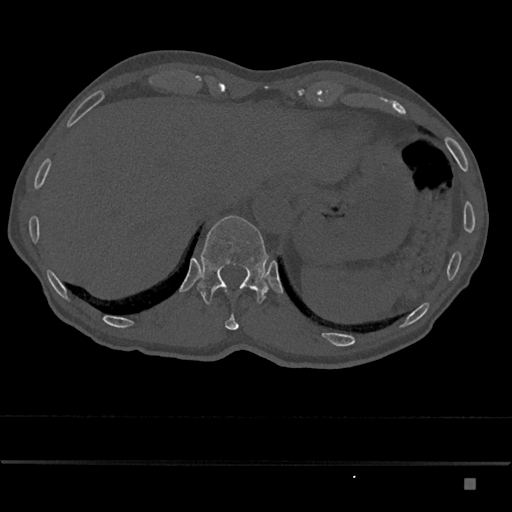
CT including the spine, one axial slice; slice 631 of 797 in the series (ordered by position); reconstruction kernel Br40s/3; bone window (W 1800 / L 400 HU); 0.5 mm slice thickness; 512 × 512 image matrix, field of view 390 × 390 mm. Male patient, age 72 years. Case-level facts recorded for this patient, not image findings: primary cancer: prostate.
Outlined on this slice (semi-automatic segmentation, software-assisted and operator-edited):
- T11 vertebra: bounding box <225,314,239,330> (left, top, right, bottom; pixels)
- T12 vertebra: <197,215,269,305>